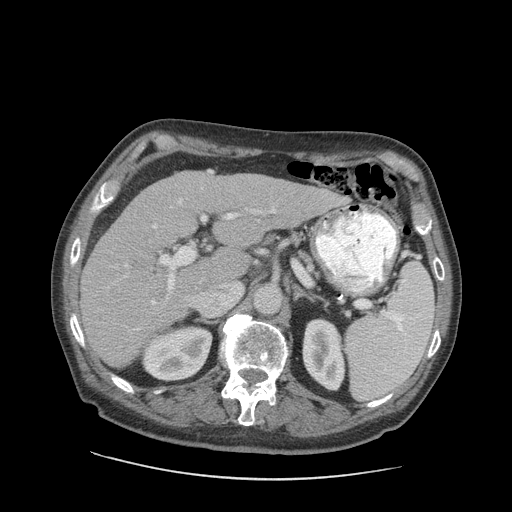
Contrast-enhanced abdominal CT (liver protocol), one axial slice; slice 53 of 89 in the series (ordered by position); reconstruction kernel STANDARD; 140 kVp; soft-tissue window (W 400 / L 40 HU); 2.5 mm slice thickness; 512 × 512 image matrix, field of view 420 × 420 mm. Case-level facts recorded for this patient, not image findings: diagnosis: hepatocellular carcinoma (patient treated with transarterial chemoembolisation; whether this scan precedes or follows treatment is not stated here); TNM stage (as recorded): Stage-I; Child-Pugh class: A; tumour nodularity: uninodular; tumour size: 4.6 cm.
Annotated regions visible in this slice (semi-automatic segmentation, software-assisted and operator-edited):
- liver parenchyma outside the tumour (the mass and vessels are separate outlines, so this box may not span the whole liver): bounding box (x1, y1, x2, y2) in pixels: (80, 170, 341, 368)
- liver vessels: (108, 170, 334, 332)